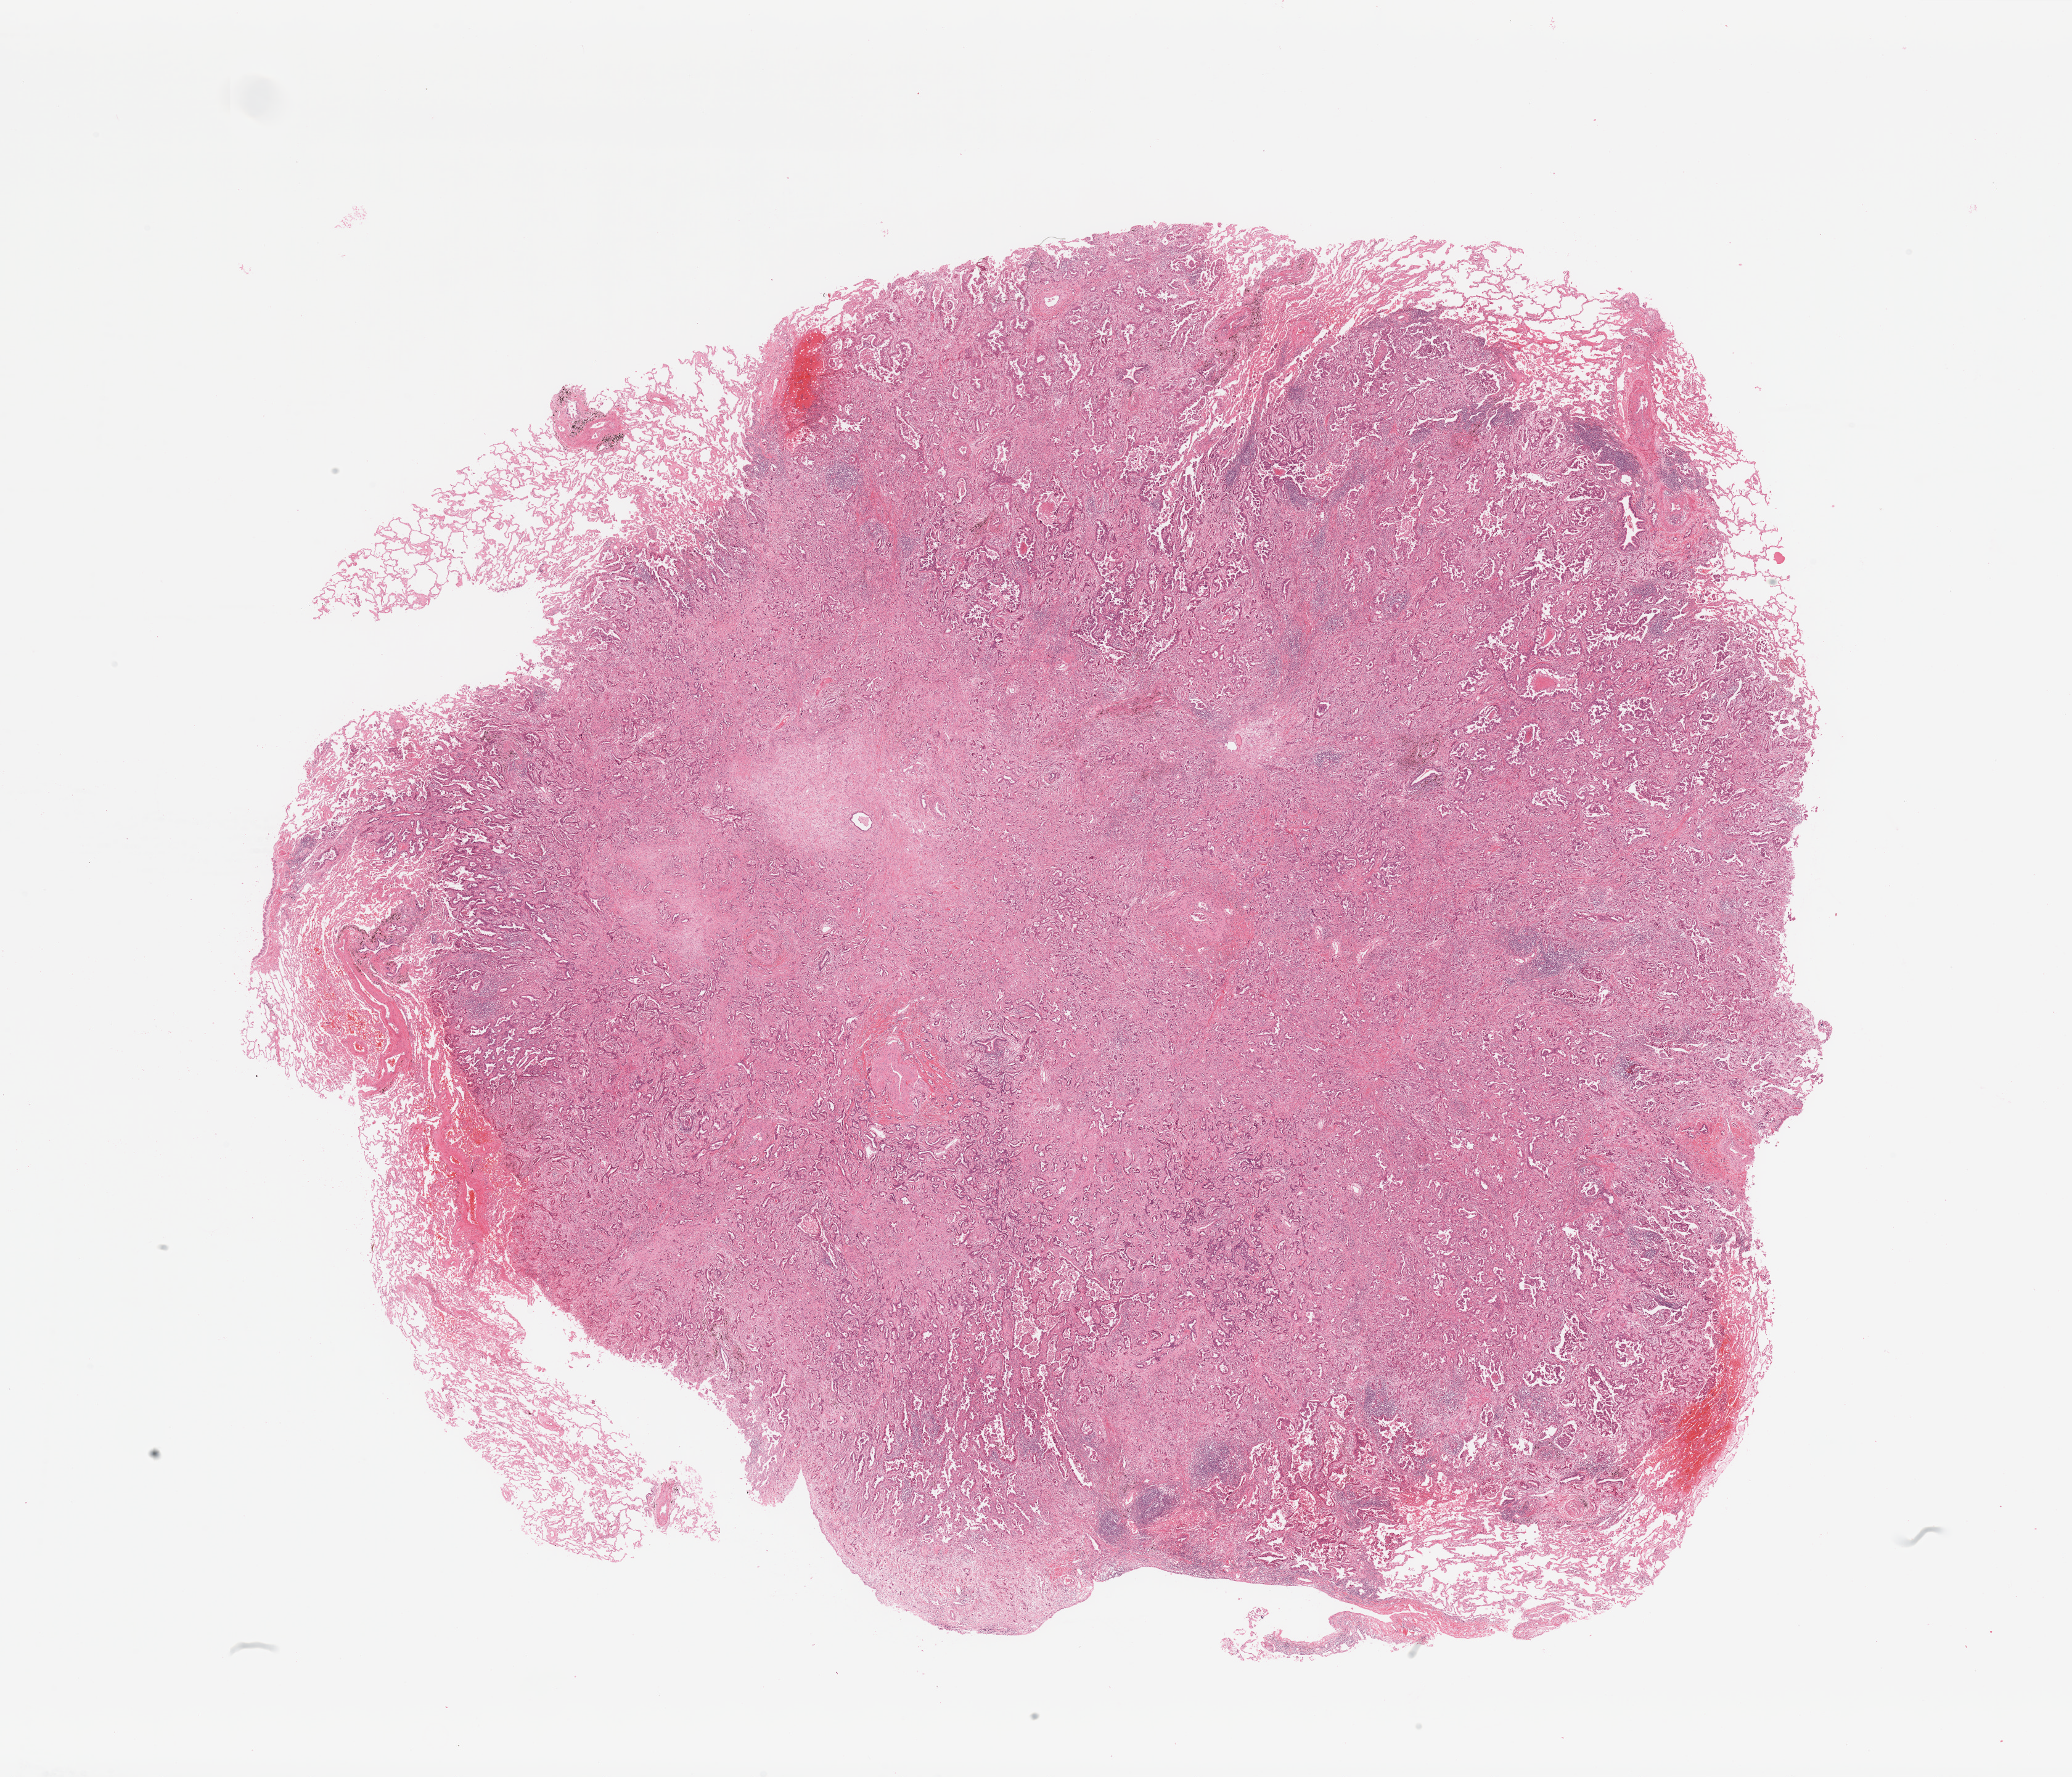
Whole-slide histology image, H&E-stained, whole scanned area (about 26.6 x 22.8 mm, from a 20x scan) shown as a low-resolution overview, lung, tumour tissue. 65-year-old female patient. Histologic grade: G3 (poorly differentiated).
• histologic diagnosis: Adenocarcinoma, NOS
• AJCC pathologic stage: IB